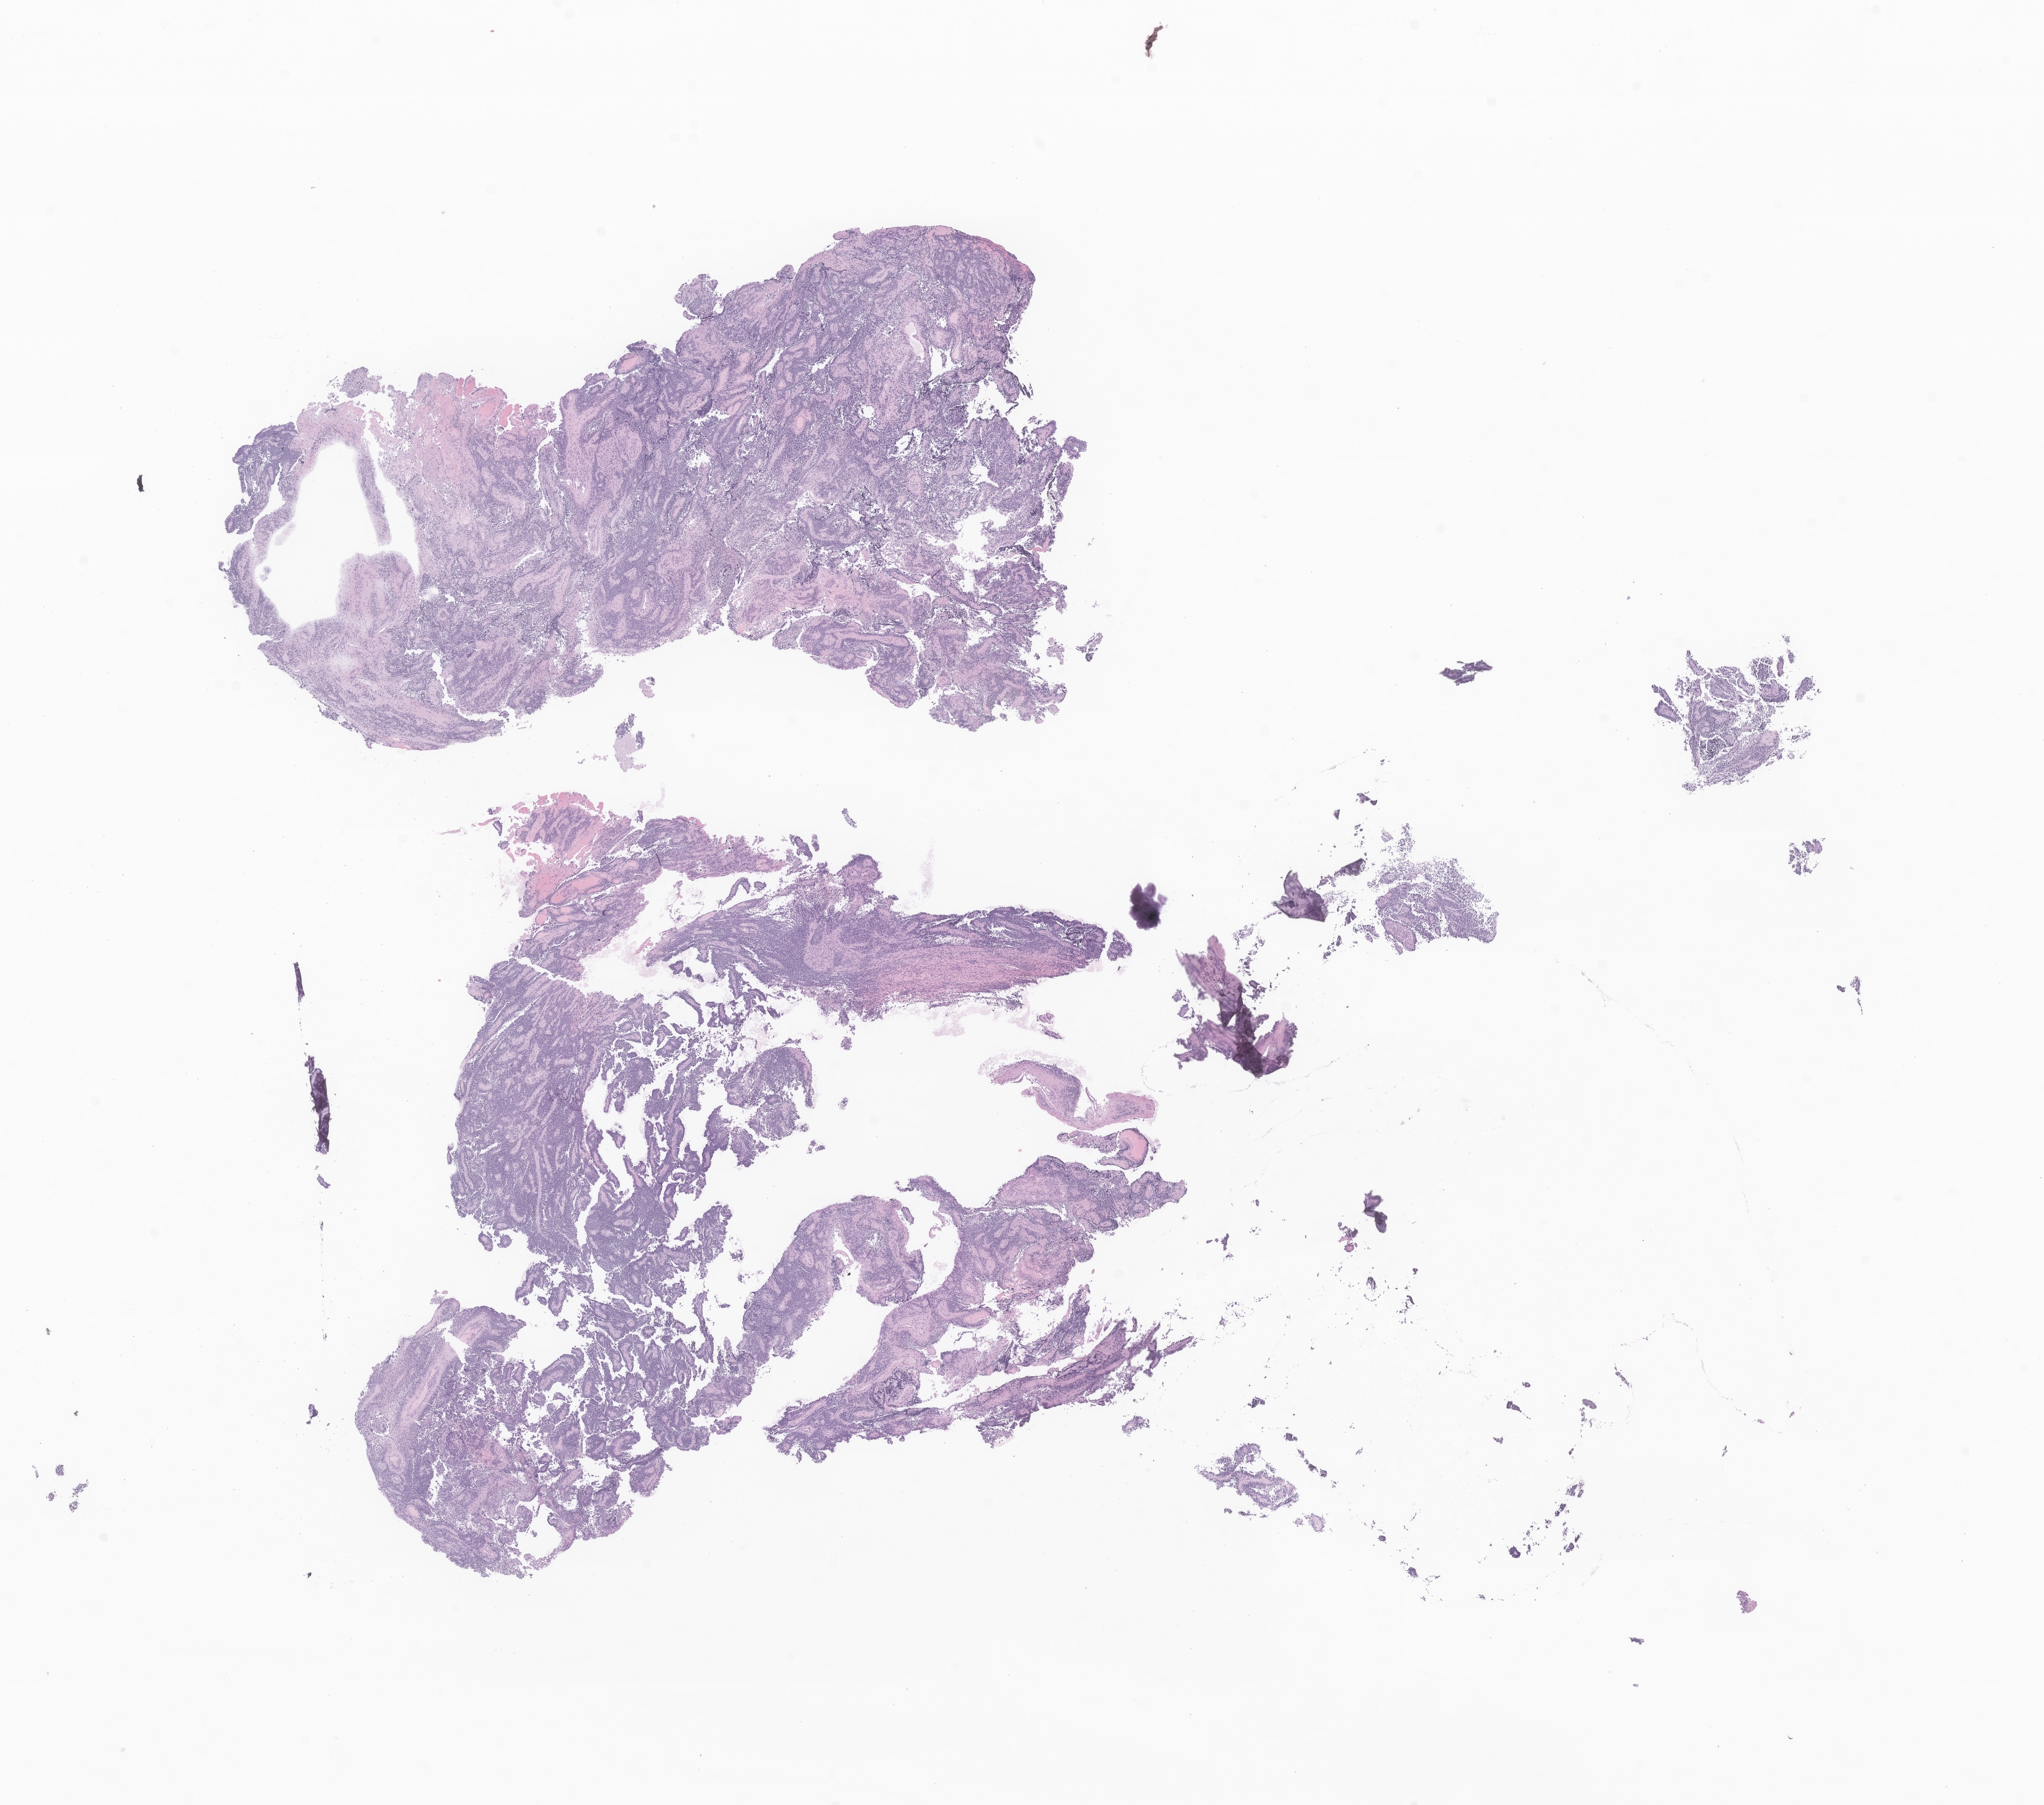
Haematoxylin and eosin whole-slide image of tumor tissue from the cerebral ventricle — whole scanned area (about 17.9 x 15.8 mm) shown as a low-resolution overview. Formalin-fixed, paraffin-embedded (FFPE) tissue. Patient male; age 62 months.
• recorded diagnosis: Ependymoma, anaplastic